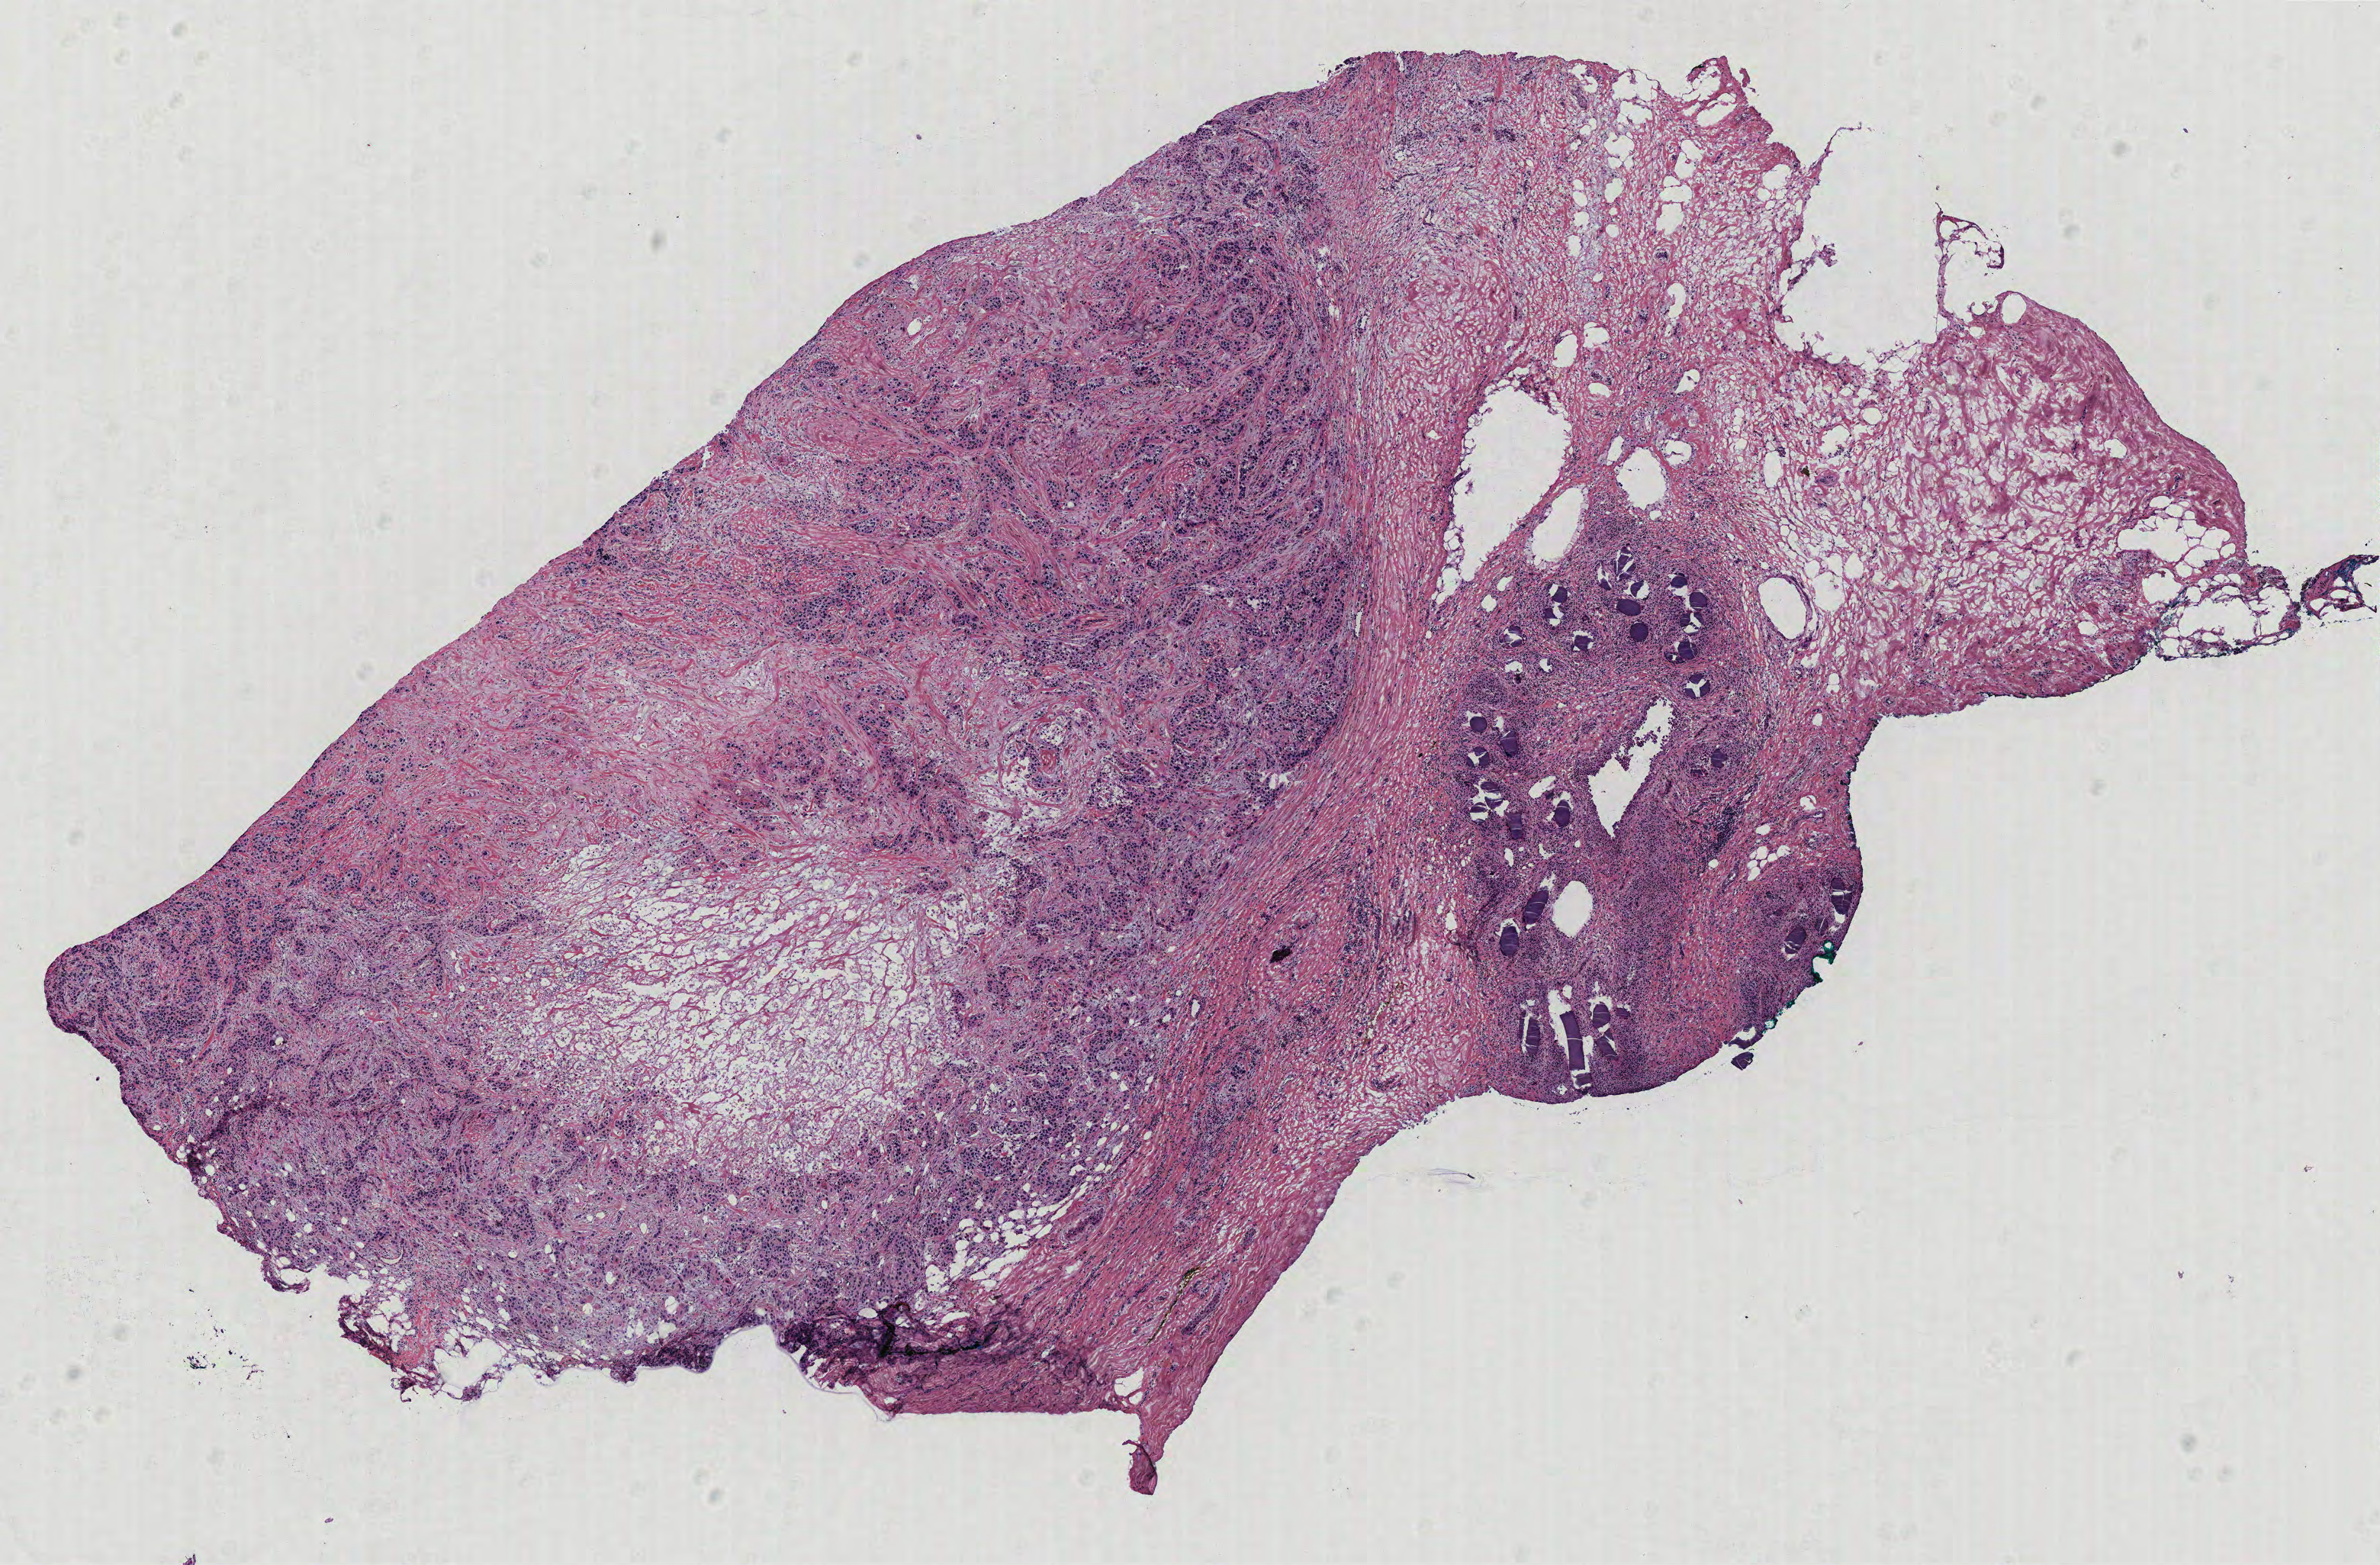
Hematoxylin and eosin (H&E) stained whole-slide image — a low-resolution overview of the entire scanned area, about 12.5 x 8.2 mm. Breast, tissue type not recorded.
* patient diagnosis (cohort enrolment): breast cancer (breast)